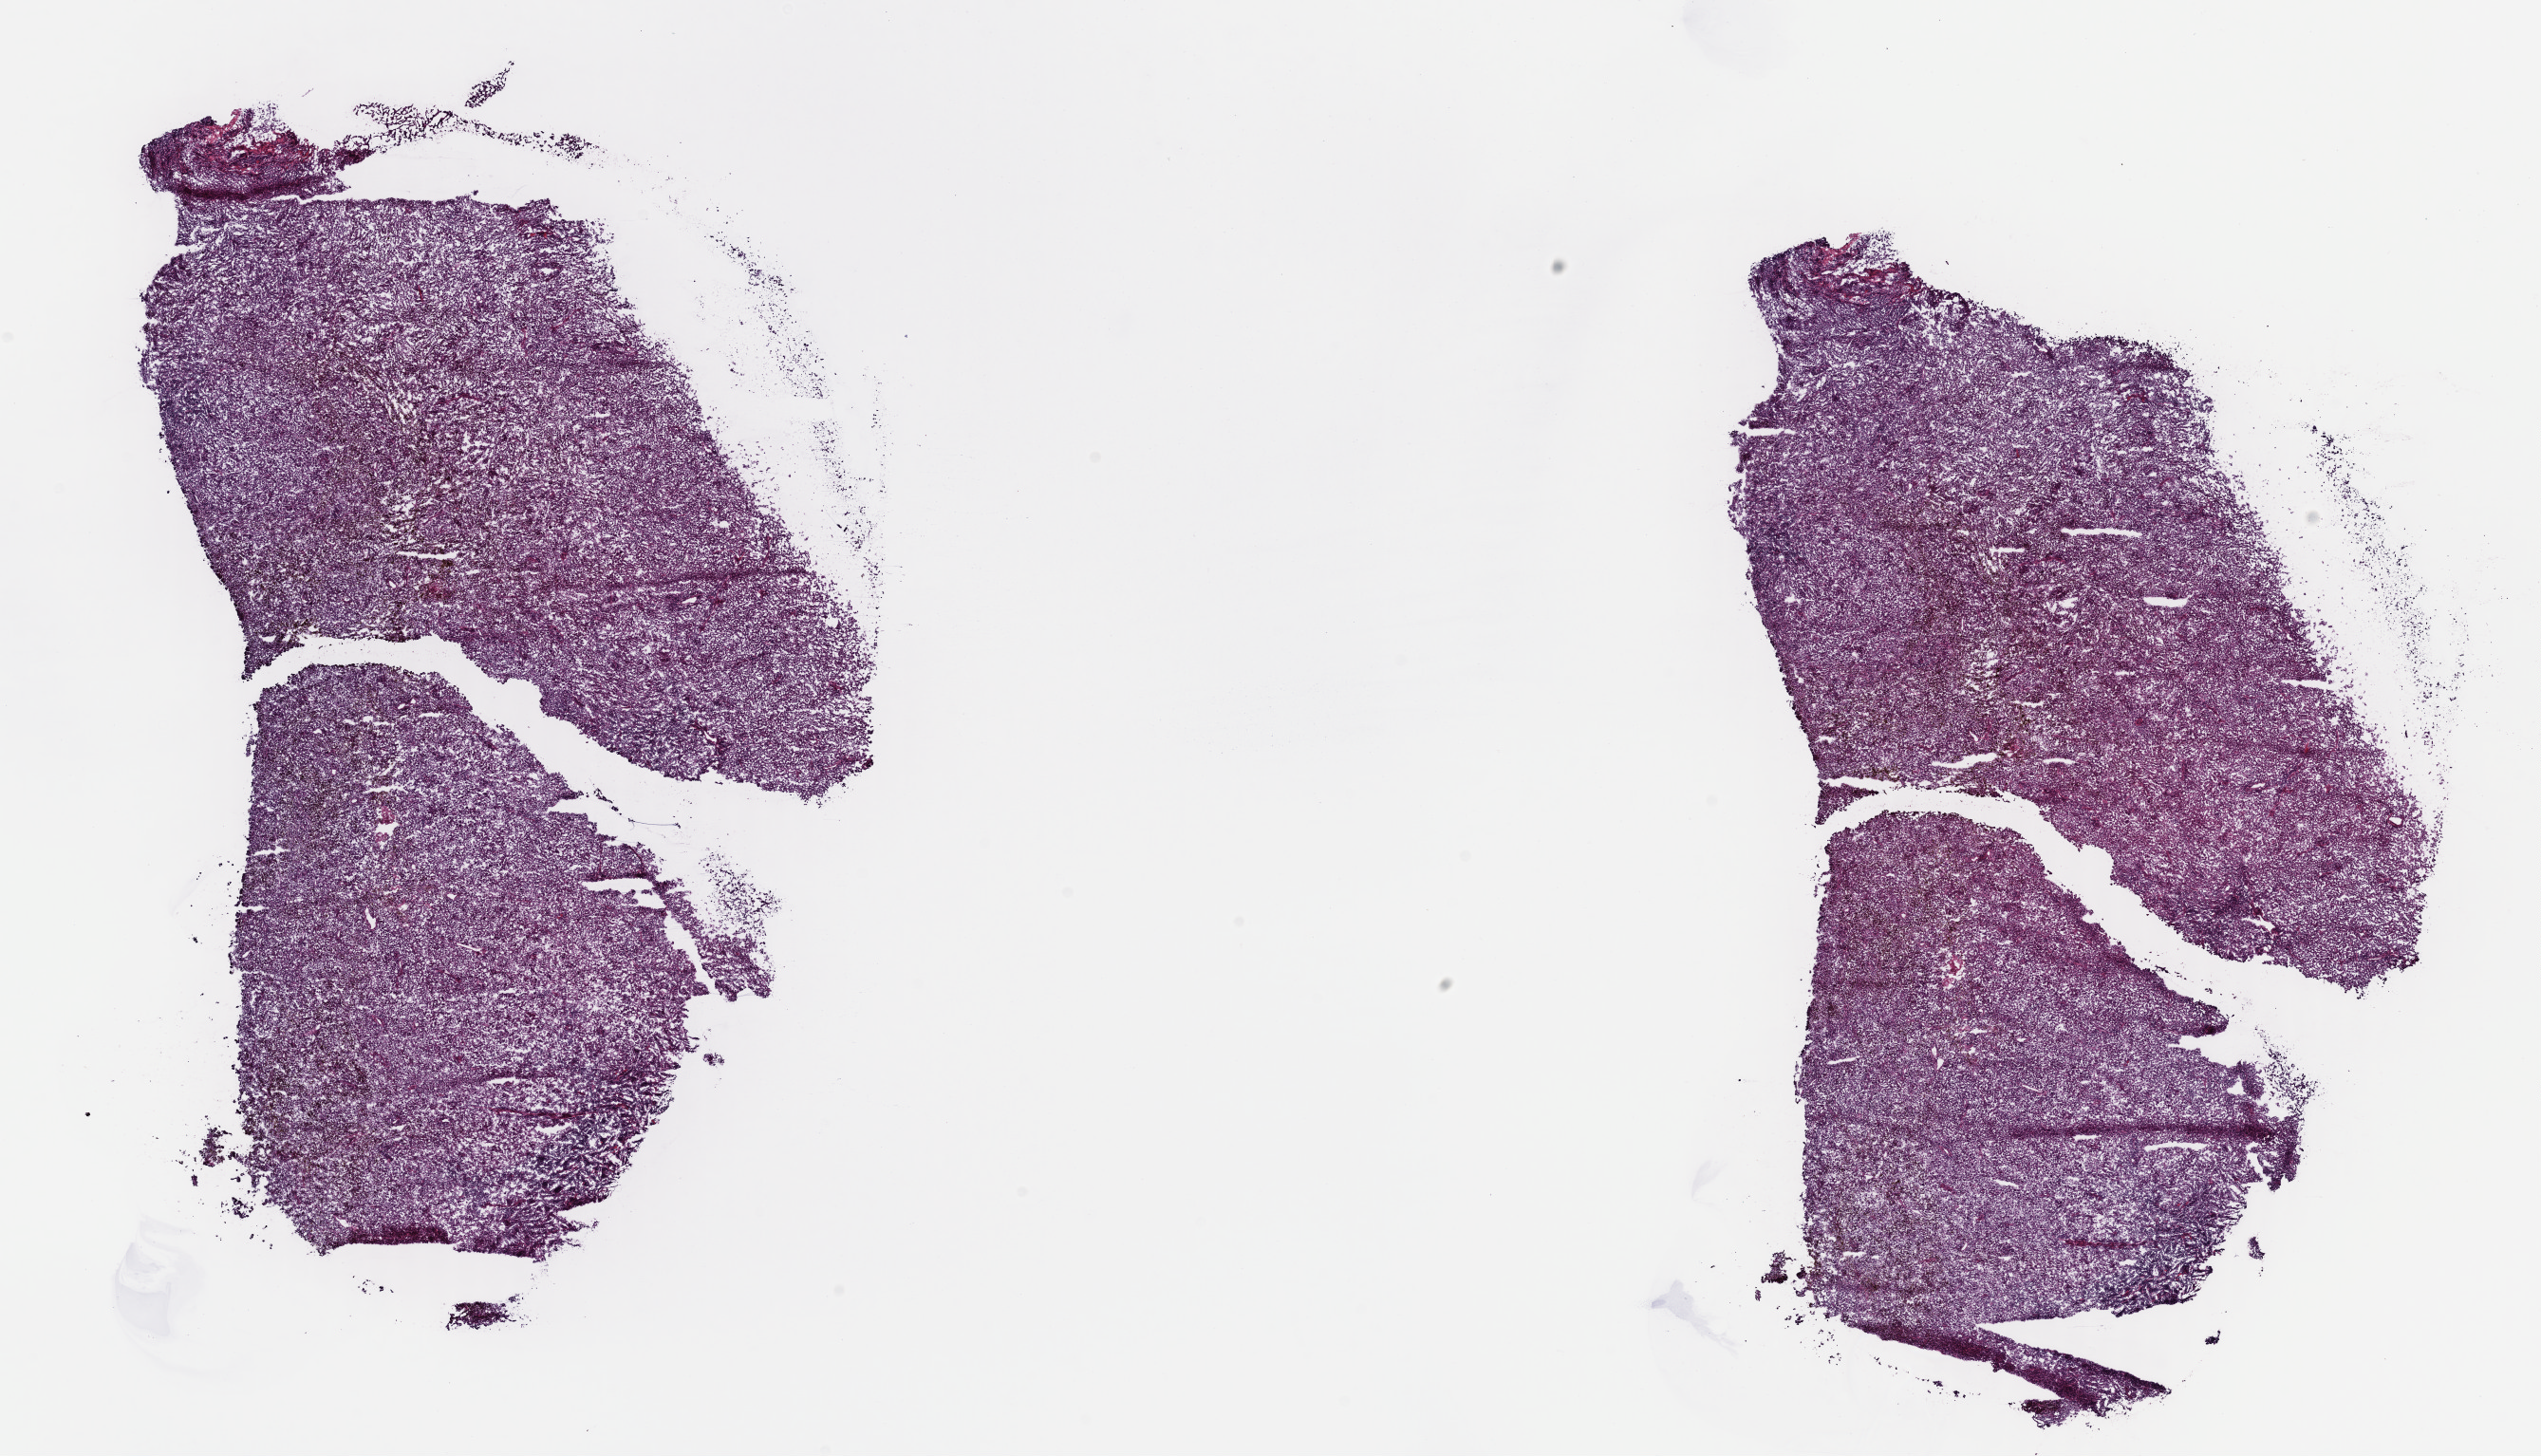
Digitized H&E tissue section (whole slide) — a low-resolution overview of the entire scanned area, about 21.1 x 12.1 mm (acquisition: 40x scan). Frozen section from the top of the tissue portion. Metastatic tumour sample, sampled site: lymph node. Female patient; age at initial diagnosis 75 years. Composition of this section per pathologist review: tumour cells 85%, tumour nuclei 85%, normal cells 0%, stromal cells 14%, necrosis 1%. Infiltration values recorded for this section: lymphocyte infiltration 3%, monocyte infiltration 1%, neutrophil infiltration 0%.
This section: metastatic tumour tissue. Patient diagnosis: Malignant melanoma, NOS.